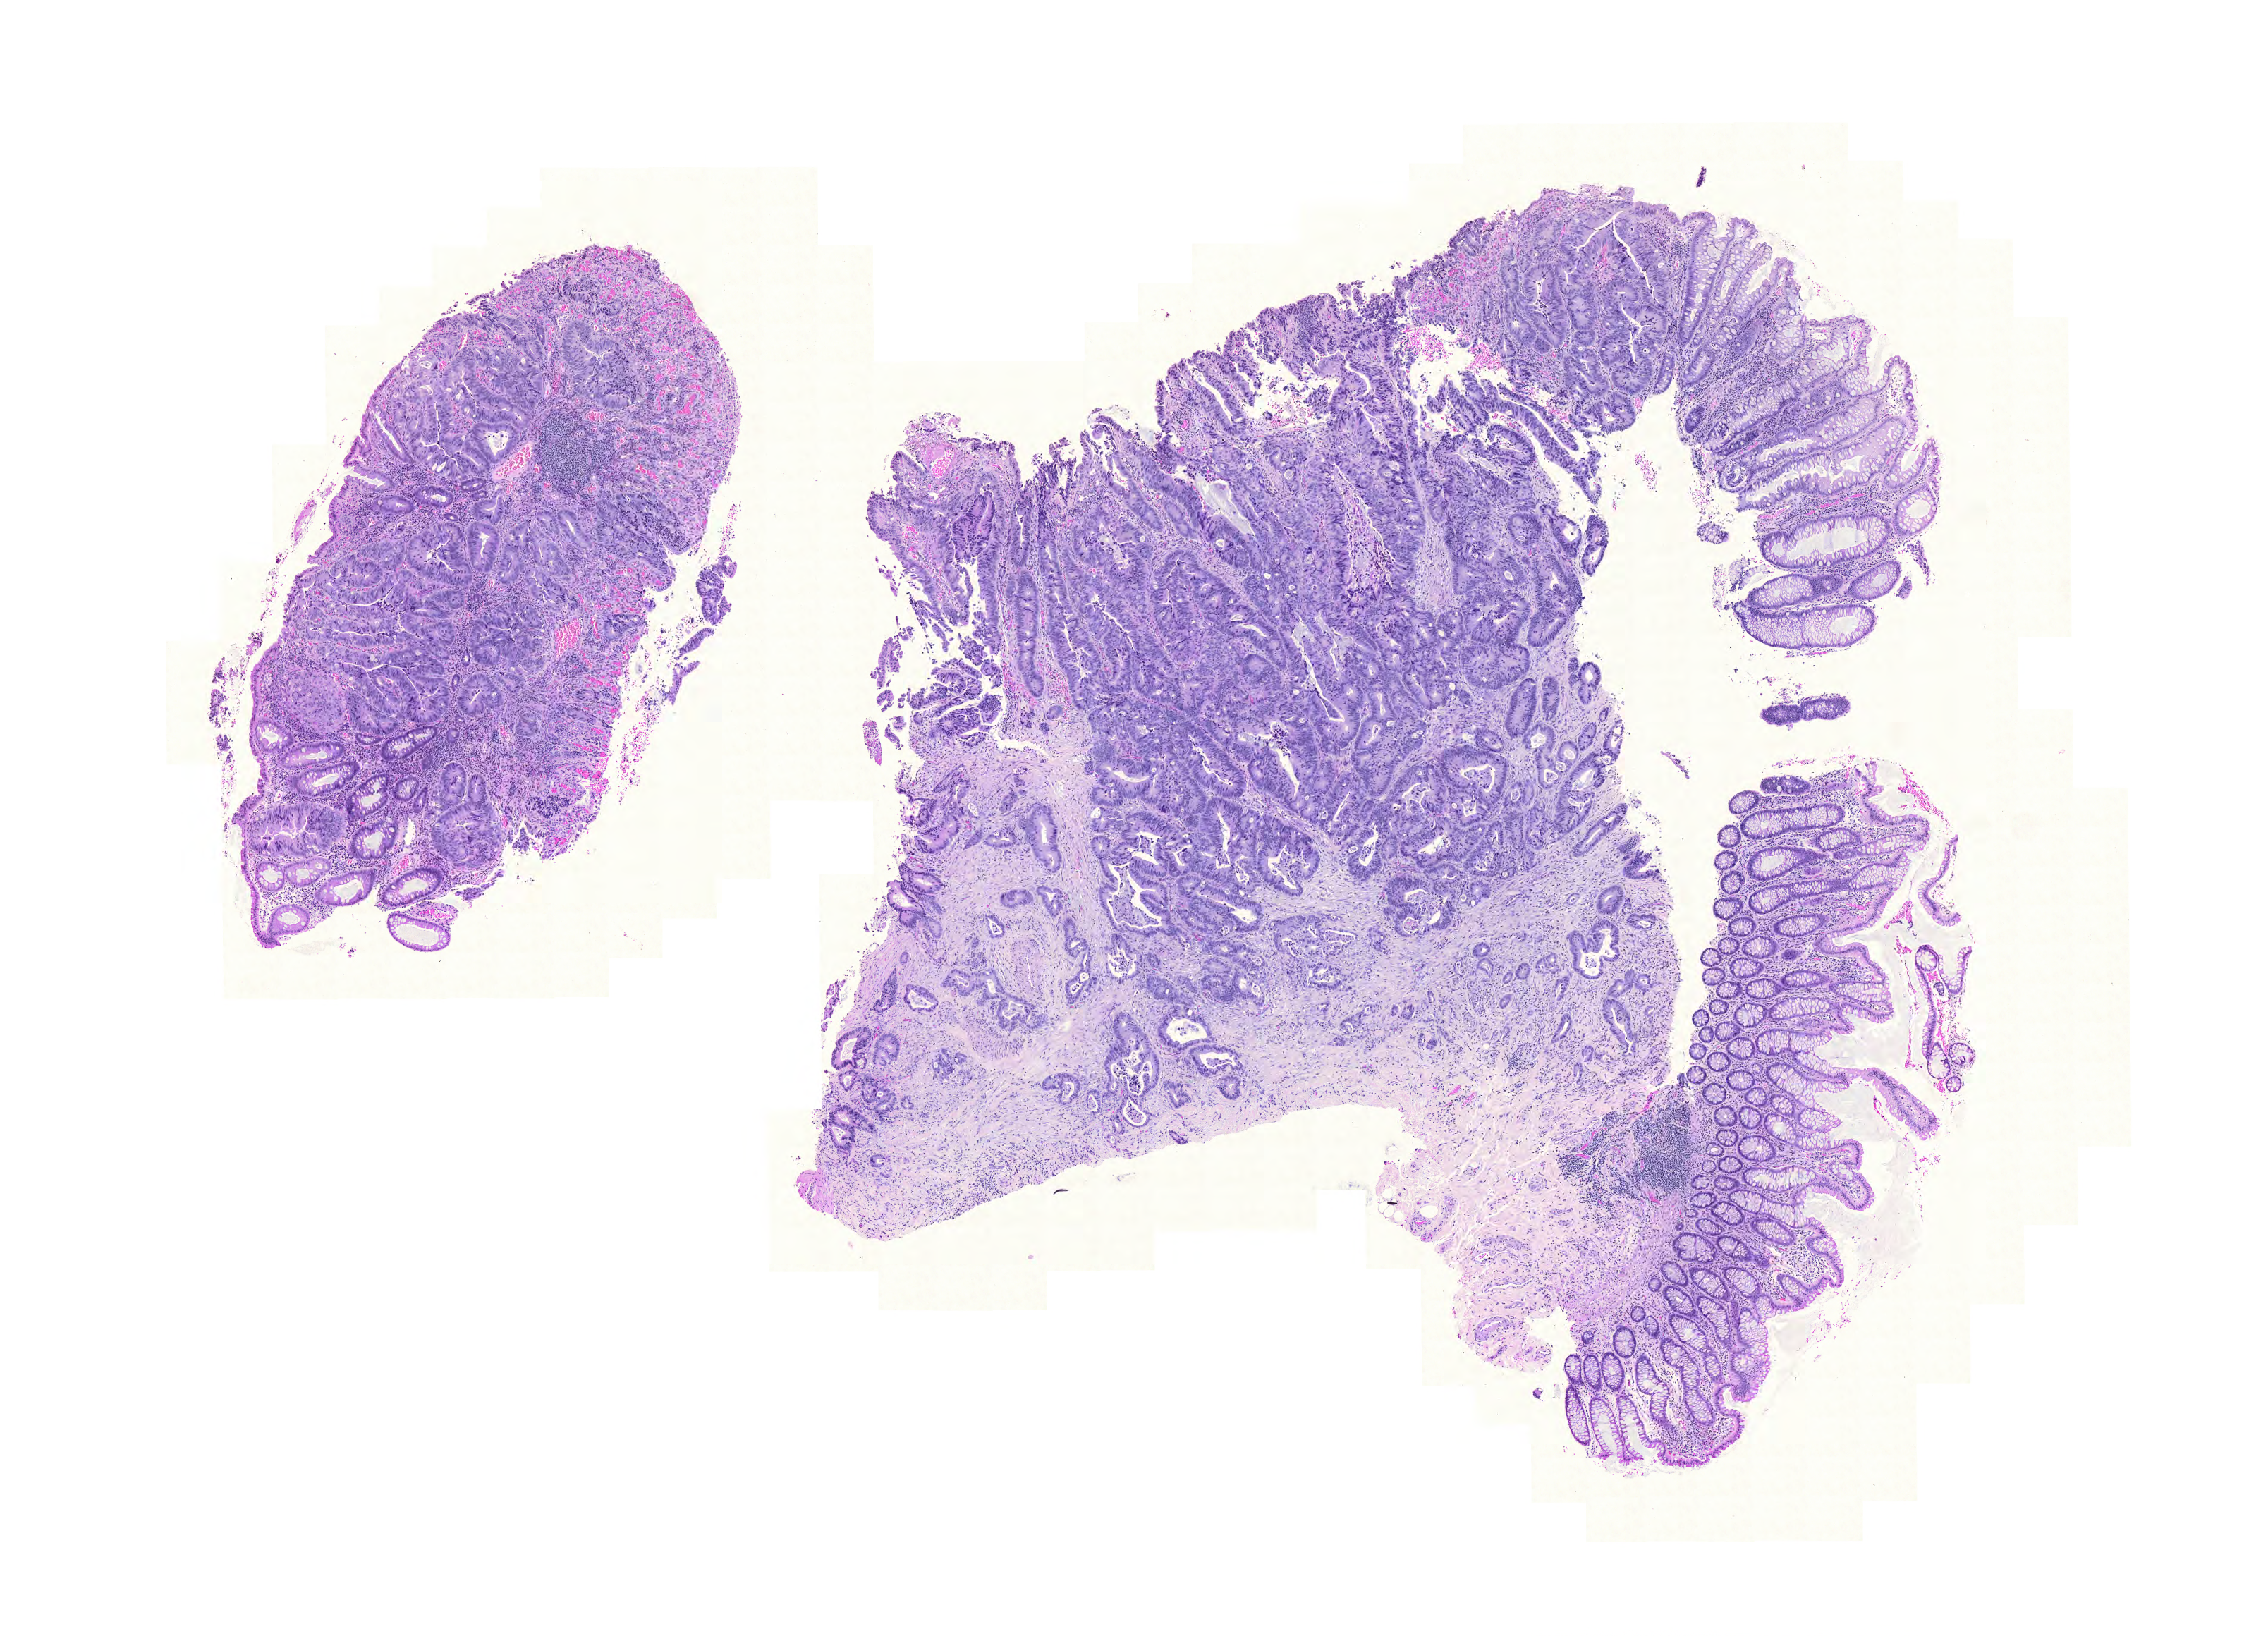
Whole-slide histology image, H&E-stained — whole scanned area (about 12.0 x 8.6 mm, from a 20x scan) shown as a low-resolution overview. Formalin-fixed paraffin-embedded (FFPE) diagnostic section. Primary tumour sample from the rectum. Female patient; age at initial diagnosis 69 years.
TNM: T3 N1 M0. AJCC pathologic stage: IIIB (6th edition). Lymph nodes positive (case pathology): 3 of 35 examined. Histologic diagnosis: Adenocarcinoma, NOS (rectosigmoid junction).